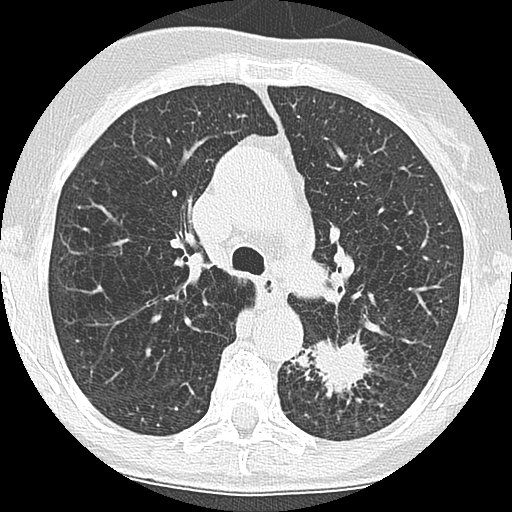
Low-dose screening chest CT, one axial slice. Reconstruction kernel LUNG. 120 kVp. Lung window (W 1500 / L -600 HU). 2.5 mm slice thickness. 512 × 512 image matrix.
Annotated regions visible in this slice (outlined manually by an expert reader):
- lesion 1 (tumor, lower lobe of left lung): bounding box (x1, y1, x2, y2) in pixels: (291, 339, 370, 396)